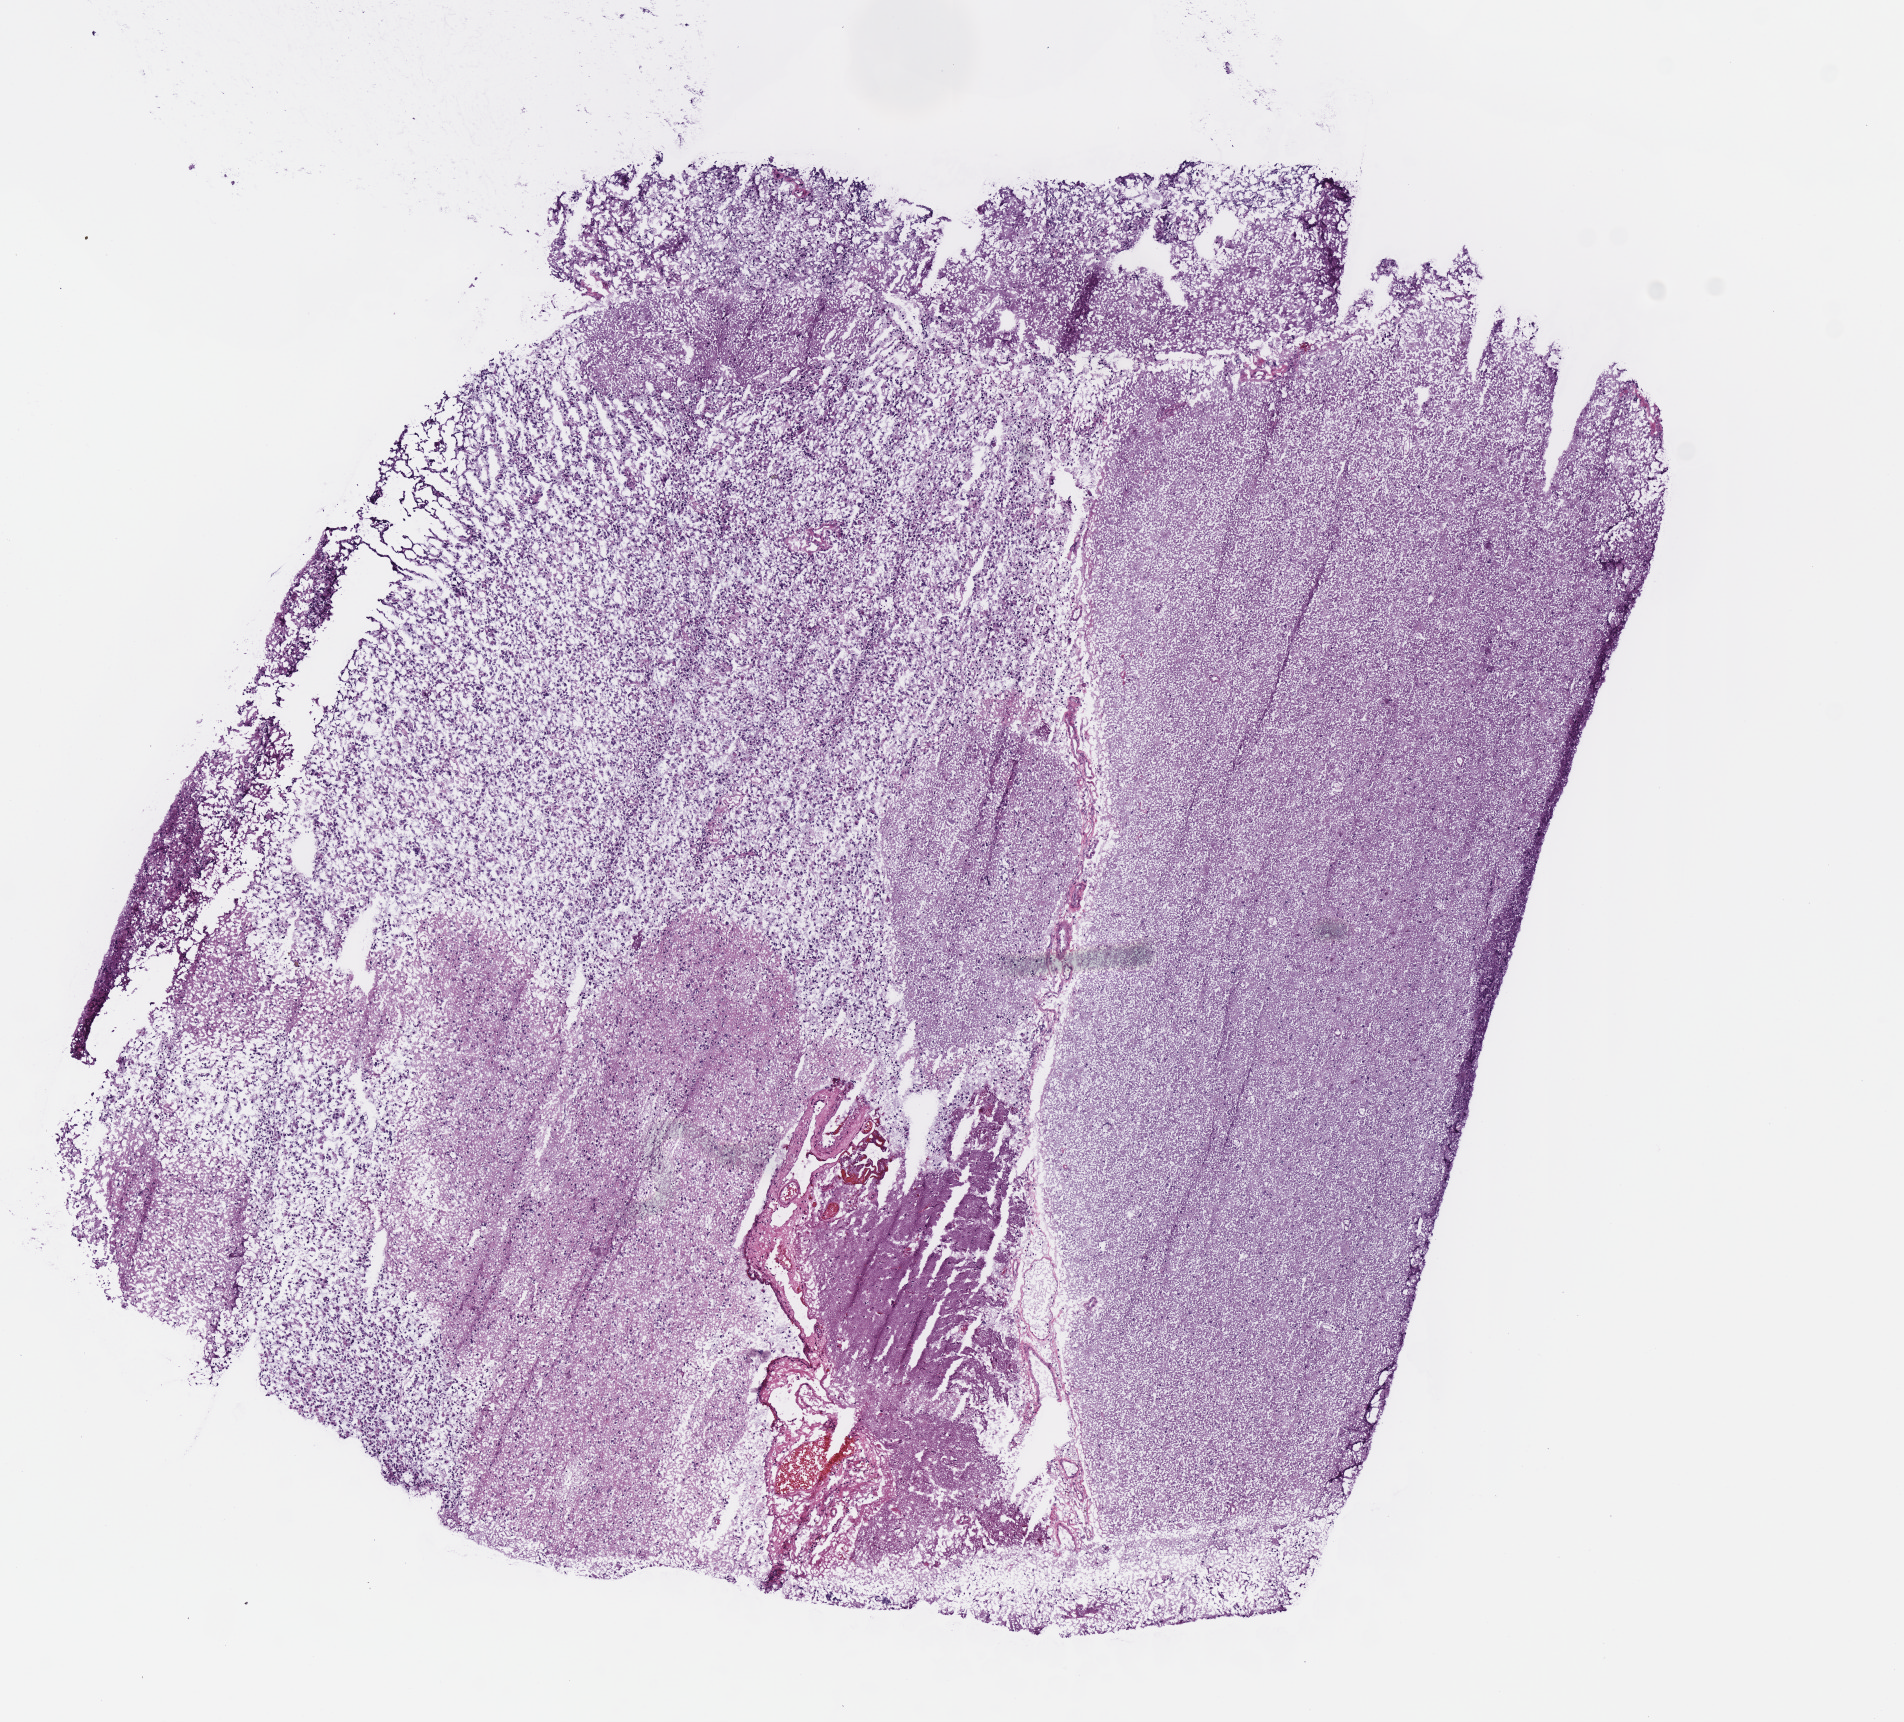
Whole-slide histology image, Hematoxylin and eosin (H&E) stained — whole scanned area (about 7.5 x 6.8 mm) shown as a low-resolution overview. Frozen section from the top of the tissue portion. Brain, primary tumour sample. Male patient; age at initial diagnosis 59 years. Histologic grade: G3 (poorly differentiated). Composition of this section per pathologist review: tumour cells 70%, tumour nuclei 75%, normal cells 30%, stromal cells 0%, necrosis 0%.
• laterality: left
• pathologic diagnosis: Oligodendroglioma, anaplastic (cerebrum)